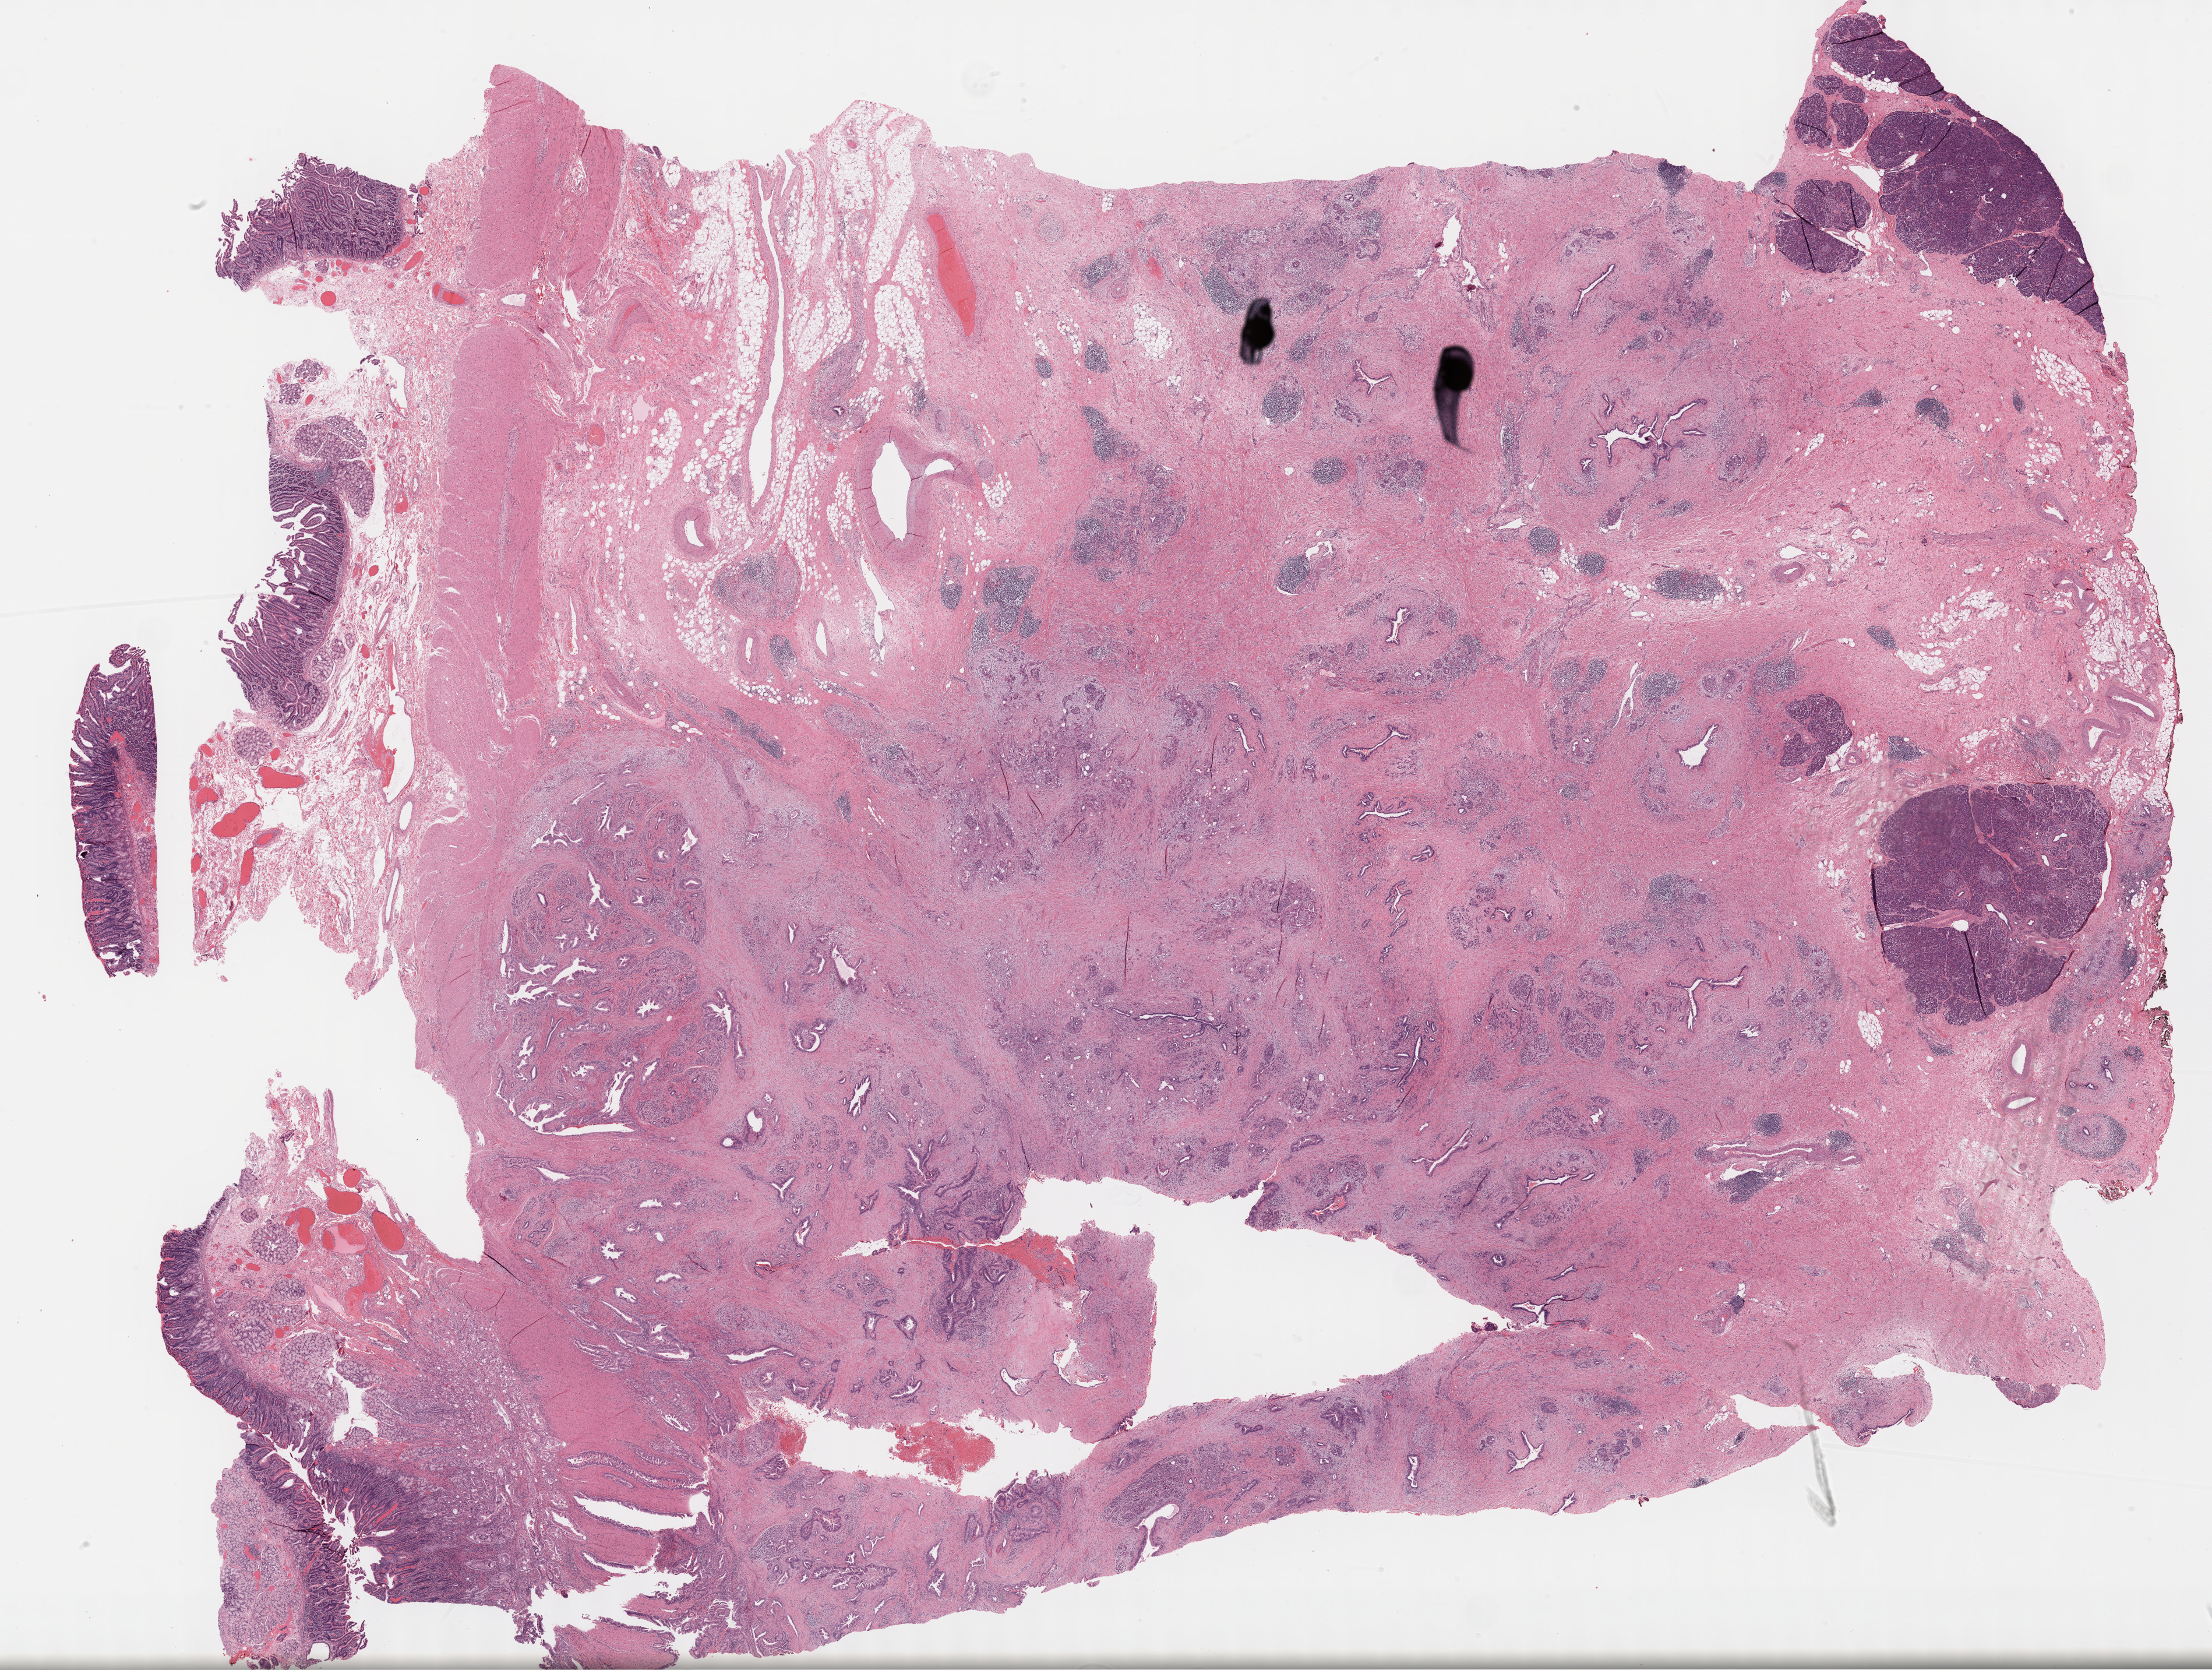
H&E-stained whole-slide image, shown as a low-resolution overview of the whole scanned area (about 30.7 x 23.2 mm, slide scanned at 40x); formalin-fixed paraffin-embedded (FFPE) diagnostic section; pancreas, primary tumour sample. Male, age 35 years at initial diagnosis. Histologic grade: G3 (poorly differentiated).
AJCC pathologic stage: IIB (7th edition). Lymph nodes positive (case pathology): 2 of 16 examined. Pathologic diagnosis: Infiltrating duct carcinoma, NOS (head of pancreas).